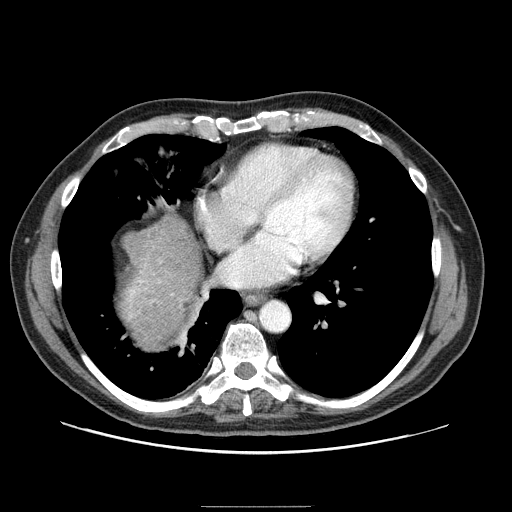
Contrast-enhanced abdominal CT (liver protocol), one axial slice; position 87 of 99 along the scan axis; reconstruction kernel STANDARD; 100 kVp; one of 2 acquisitions stored at this slice position; soft-tissue window (W 400 / L 40 HU); 512 × 512 image matrix, field of view 400 × 400 mm. Case-level facts recorded for this patient, not image findings: diagnosis: hepatocellular carcinoma (patient treated with transarterial chemoembolisation; whether this scan precedes or follows treatment is not stated here); TNM stage (as recorded): Stage-II; Child-Pugh class: A; tumour nodularity: multinodular; tumour size: 3.2 cm.
Annotated regions visible in this slice (semi-automatic segmentation, software-assisted and operator-edited):
- liver parenchyma outside the tumour (the mass and vessels are separate outlines, so this box may not span the whole liver): bounding box <122,214,200,348> (left, top, right, bottom; pixels)
- liver vessels: <130,280,143,317>